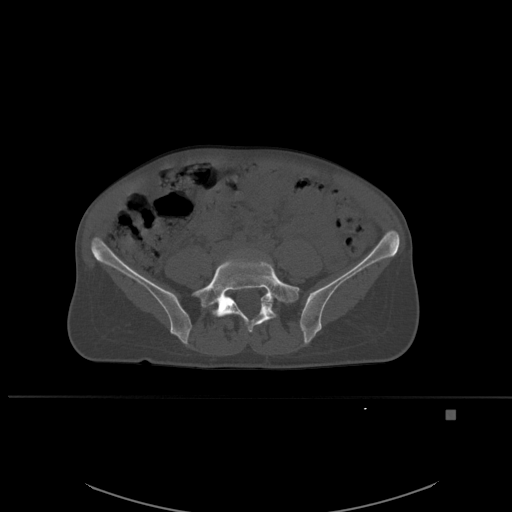
CT including the spine, one axial slice; position 174 of 537 along the scan axis; bone window (W 1800 / L 400 HU); 1.5 mm slice thickness; 512 × 512 image matrix. Patient: female, 45 years. From the clinical record (not read from this slice): primary cancer: lung.
Annotated regions visible in this slice (semi-automatically segmented with operator editing):
- L5 vertebra: bounding box (x1, y1, x2, y2) in pixels: (196, 256, 300, 332)